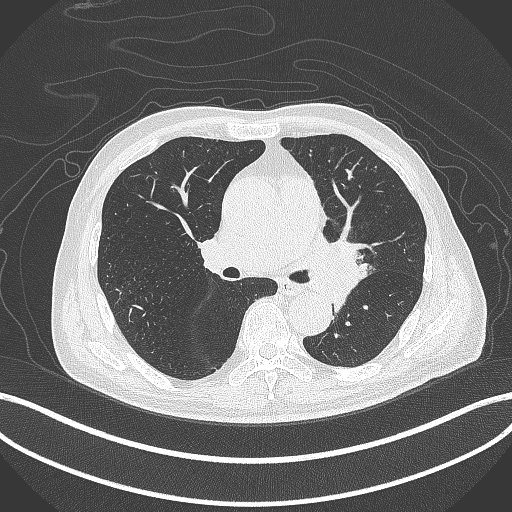
Chest CT, one axial slice. Position 250 of 417 along the scan axis. Reconstruction kernel B70f. Lung window (W 1500 / L -600 HU). 1 mm slice thickness. 512 × 512 image matrix, field of view 400 × 400 mm. Patient: male, 77 years. Case-level facts recorded for this patient, not image findings: clinical TNM (as recorded): T3 N1 M0.
Outlined on this slice (bounding box drawn by a radiologist):
- lung tumour (recorded histology: adenocarcinoma): bounding box [x1, y1, x2, y2] px = [303, 230, 370, 305]